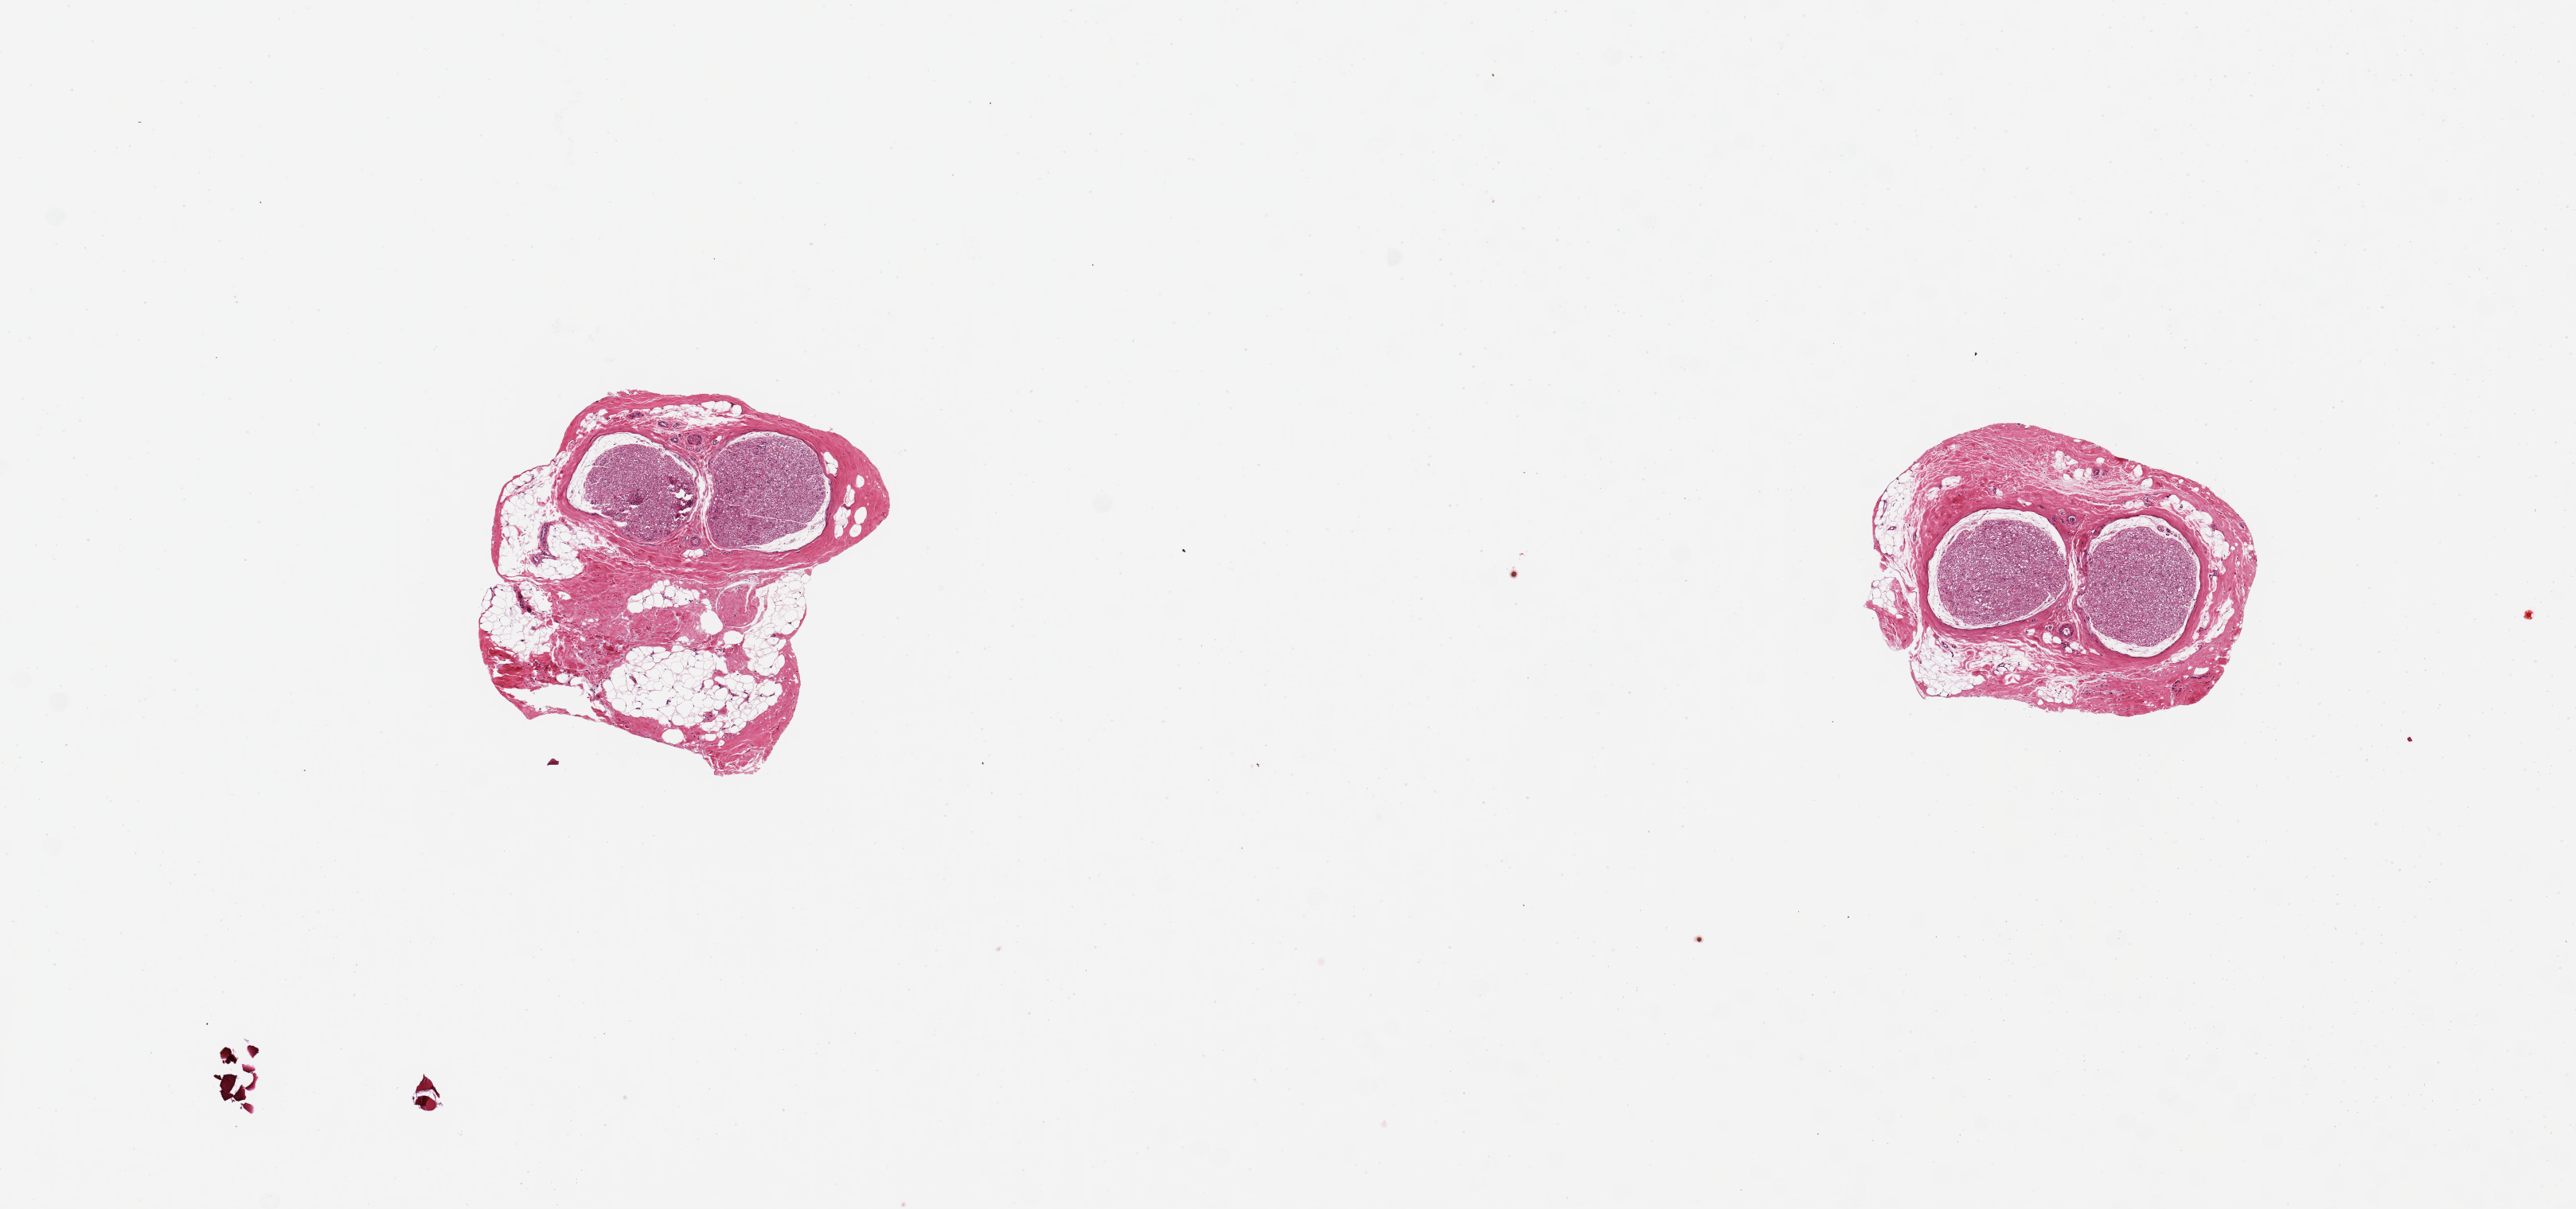
Haematoxylin and eosin whole-slide image, low-resolution overview of the scanned area, about 12.8 x 6.0 mm (slide scanned at 20x), PAXgene-fixed paraffin-embedded (PFPE) section, section of tibial nerve (target tissue), donor tissue sample. Female donor.
Pathologist's review note for this sample: 2 pieces ~1.6 mm in diameter; 60 & 40% adjacent adipose and fibrous stroma.